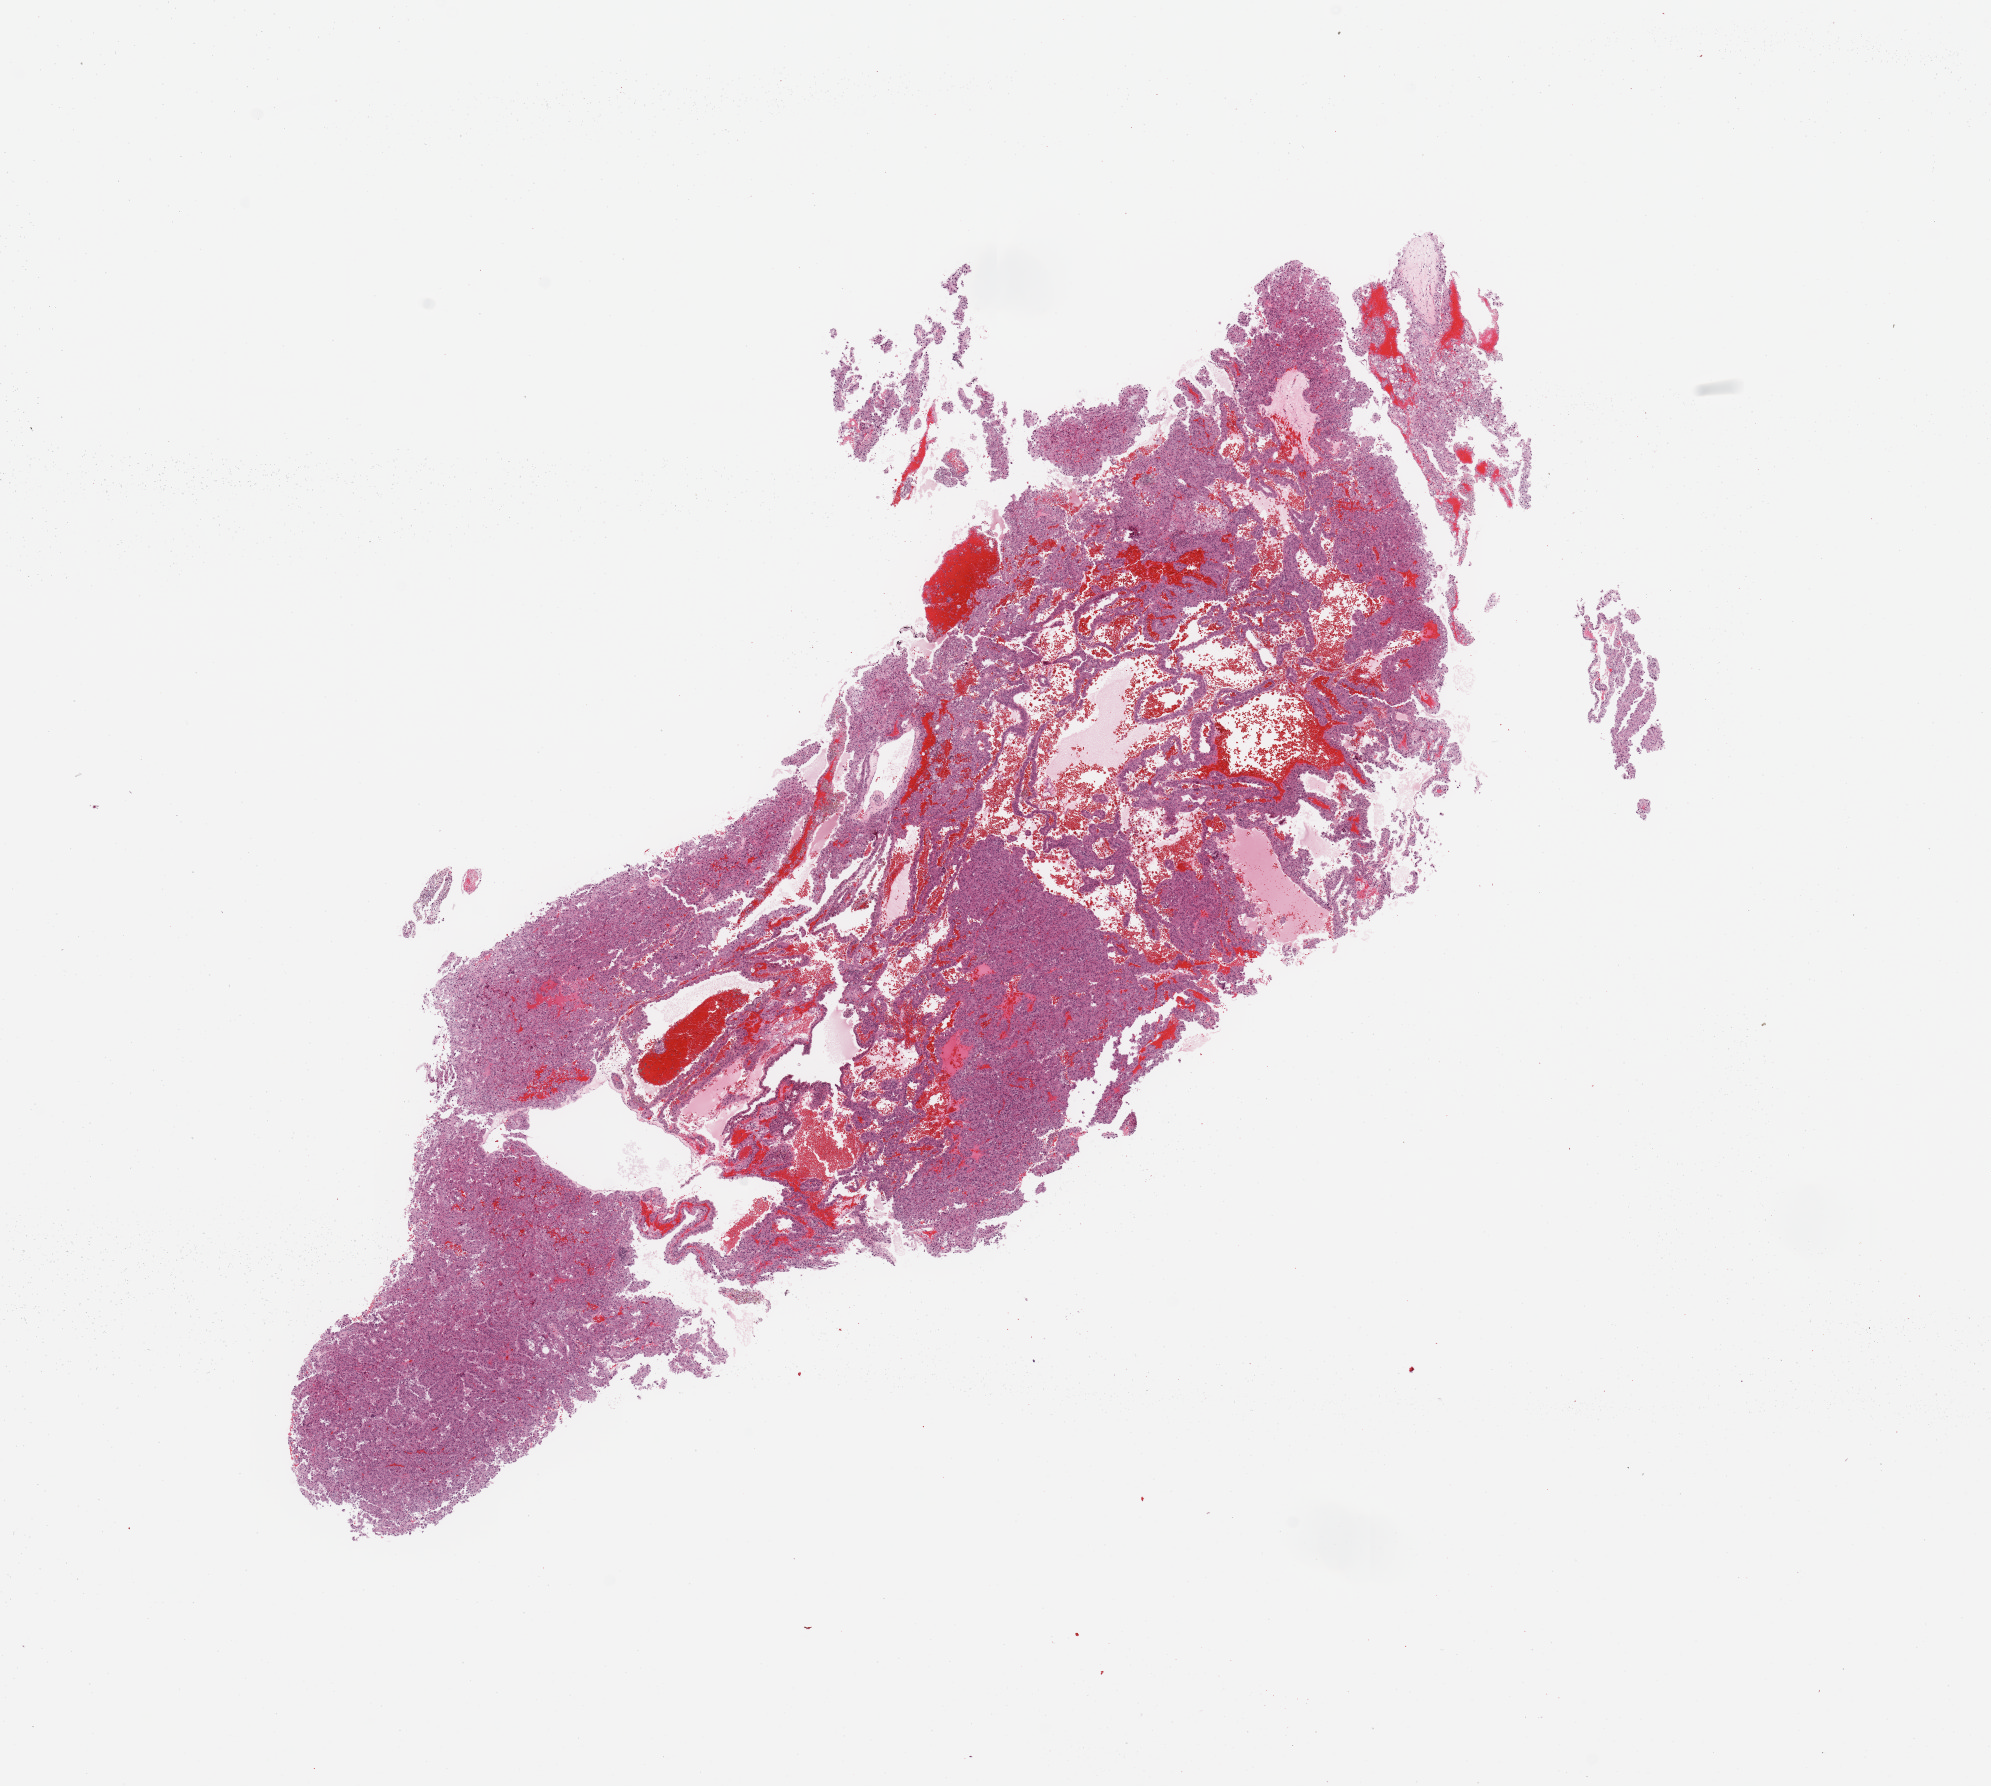
Hematoxylin and eosin (H&E) stained whole-slide image — low-resolution overview of the scanned area, about 15.8 x 14.1 mm (acquisition: 20x scan). Tumour tissue sample, sampled site: kidney. Patient: female, age 68 years. Histologic grade: G4 (undifferentiated). Composition of this section per pathologist review: tumour nuclei 90%, necrosis 2%.
- diagnosis: Renal cell carcinoma, NOS
- primary tumour site (as recorded): middle
- AJCC pathologic stage: I